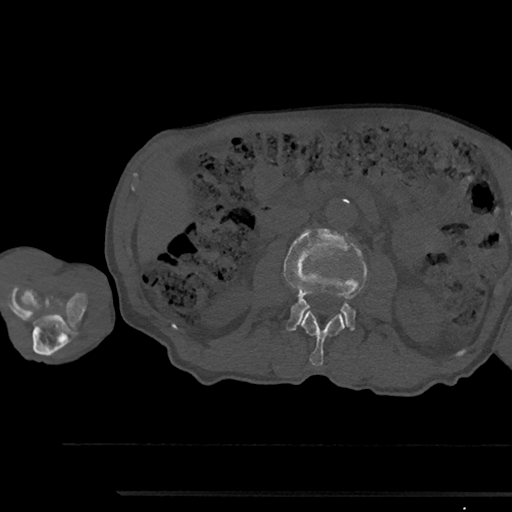
CT including the spine, one axial slice. Position 525 of 797 along the scan axis. Reconstruction kernel Br40s/3. Bone window (W 1800 / L 400 HU). 0.5 mm slice thickness. 512 × 512 image matrix. Male patient, age 79 years. Case-level facts recorded for this patient, not image findings: primary cancer: prostate.
Outlined on this slice (semi-automatically segmented with operator editing):
- L2 vertebra: bounding box [x1, y1, x2, y2] px = [301, 310, 345, 366]
- L3 vertebra: [284, 229, 368, 331]